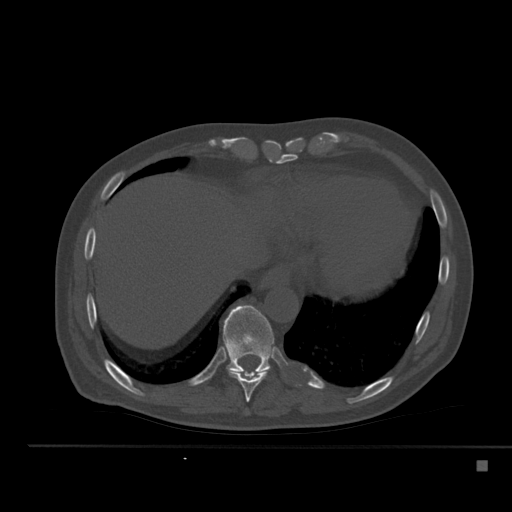
CT including the spine, one axial slice; slice 279 of 517 in the series (ordered by position); reconstruction kernel Br40s; 120 kVp; bone window (W 1800 / L 400 HU); 1.5 mm slice thickness; 512 × 512 image matrix, field of view 408 × 408 mm. Patient: male, 70 years. Case-level facts recorded for this patient, not image findings: primary cancer: renal.
Outlined on this slice (semi-automatic segmentation, software-assisted and operator-edited):
- T10 vertebra: bounding box [x1, y1, x2, y2] px = [223, 305, 276, 376]
- T9 vertebra: [227, 352, 268, 402]